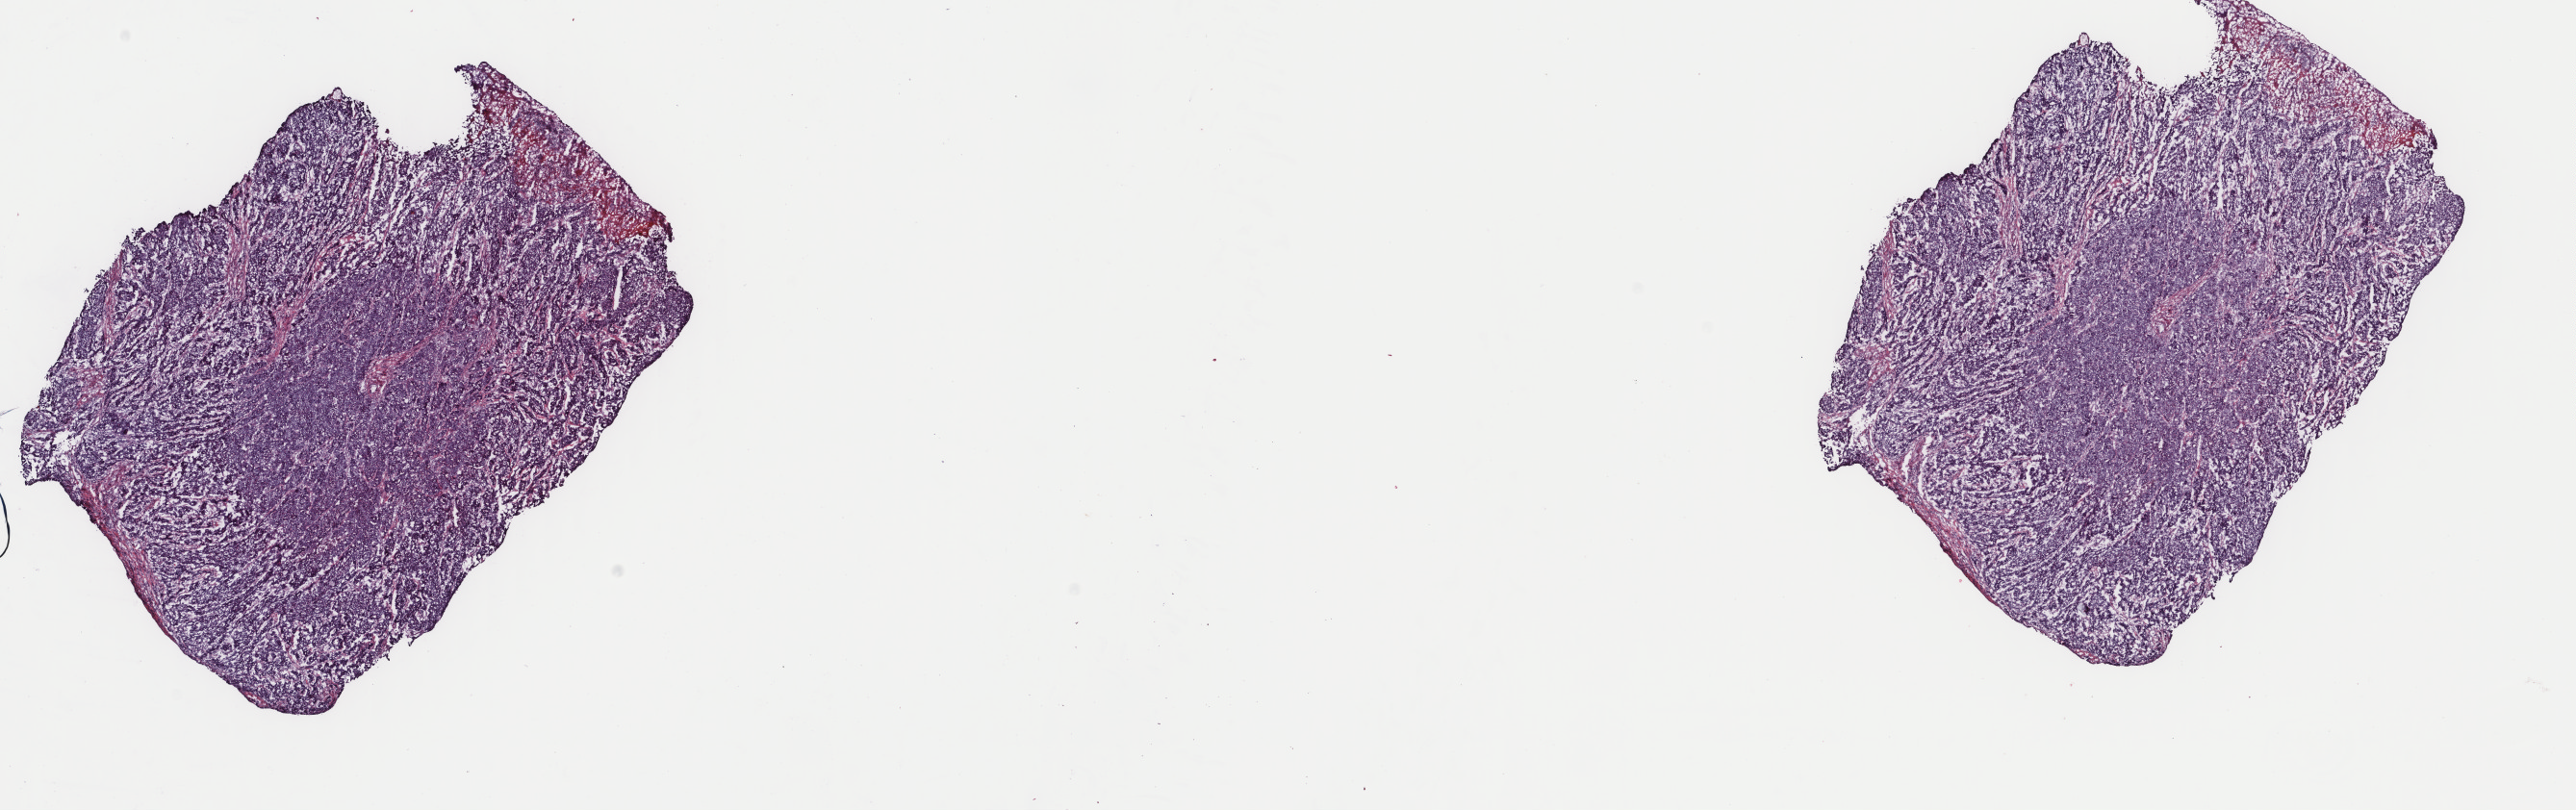
H&E-stained whole-slide image, shown as a low-resolution overview of the whole scanned area (about 21.2 x 6.7 mm, slide scanned at 40x), frozen section, sample: primary tumour, stomach. Male patient; age at initial diagnosis 73 years. Histologic grade: G3 (poorly differentiated). Composition of this section per pathologist review: tumour cells 85%, tumour nuclei 90%, normal cells 0%, stromal cells 15%, necrosis 0%. Inflammatory infiltration, as recorded: lymphocyte infiltration 0%, monocyte infiltration 0%, neutrophil infiltration 0%.
AJCC pathologic stage: IIB (7th edition). Histologic diagnosis: Carcinoma, diffuse type (gastric antrum). Lymph nodes positive (case pathology): 2 of 48 examined.